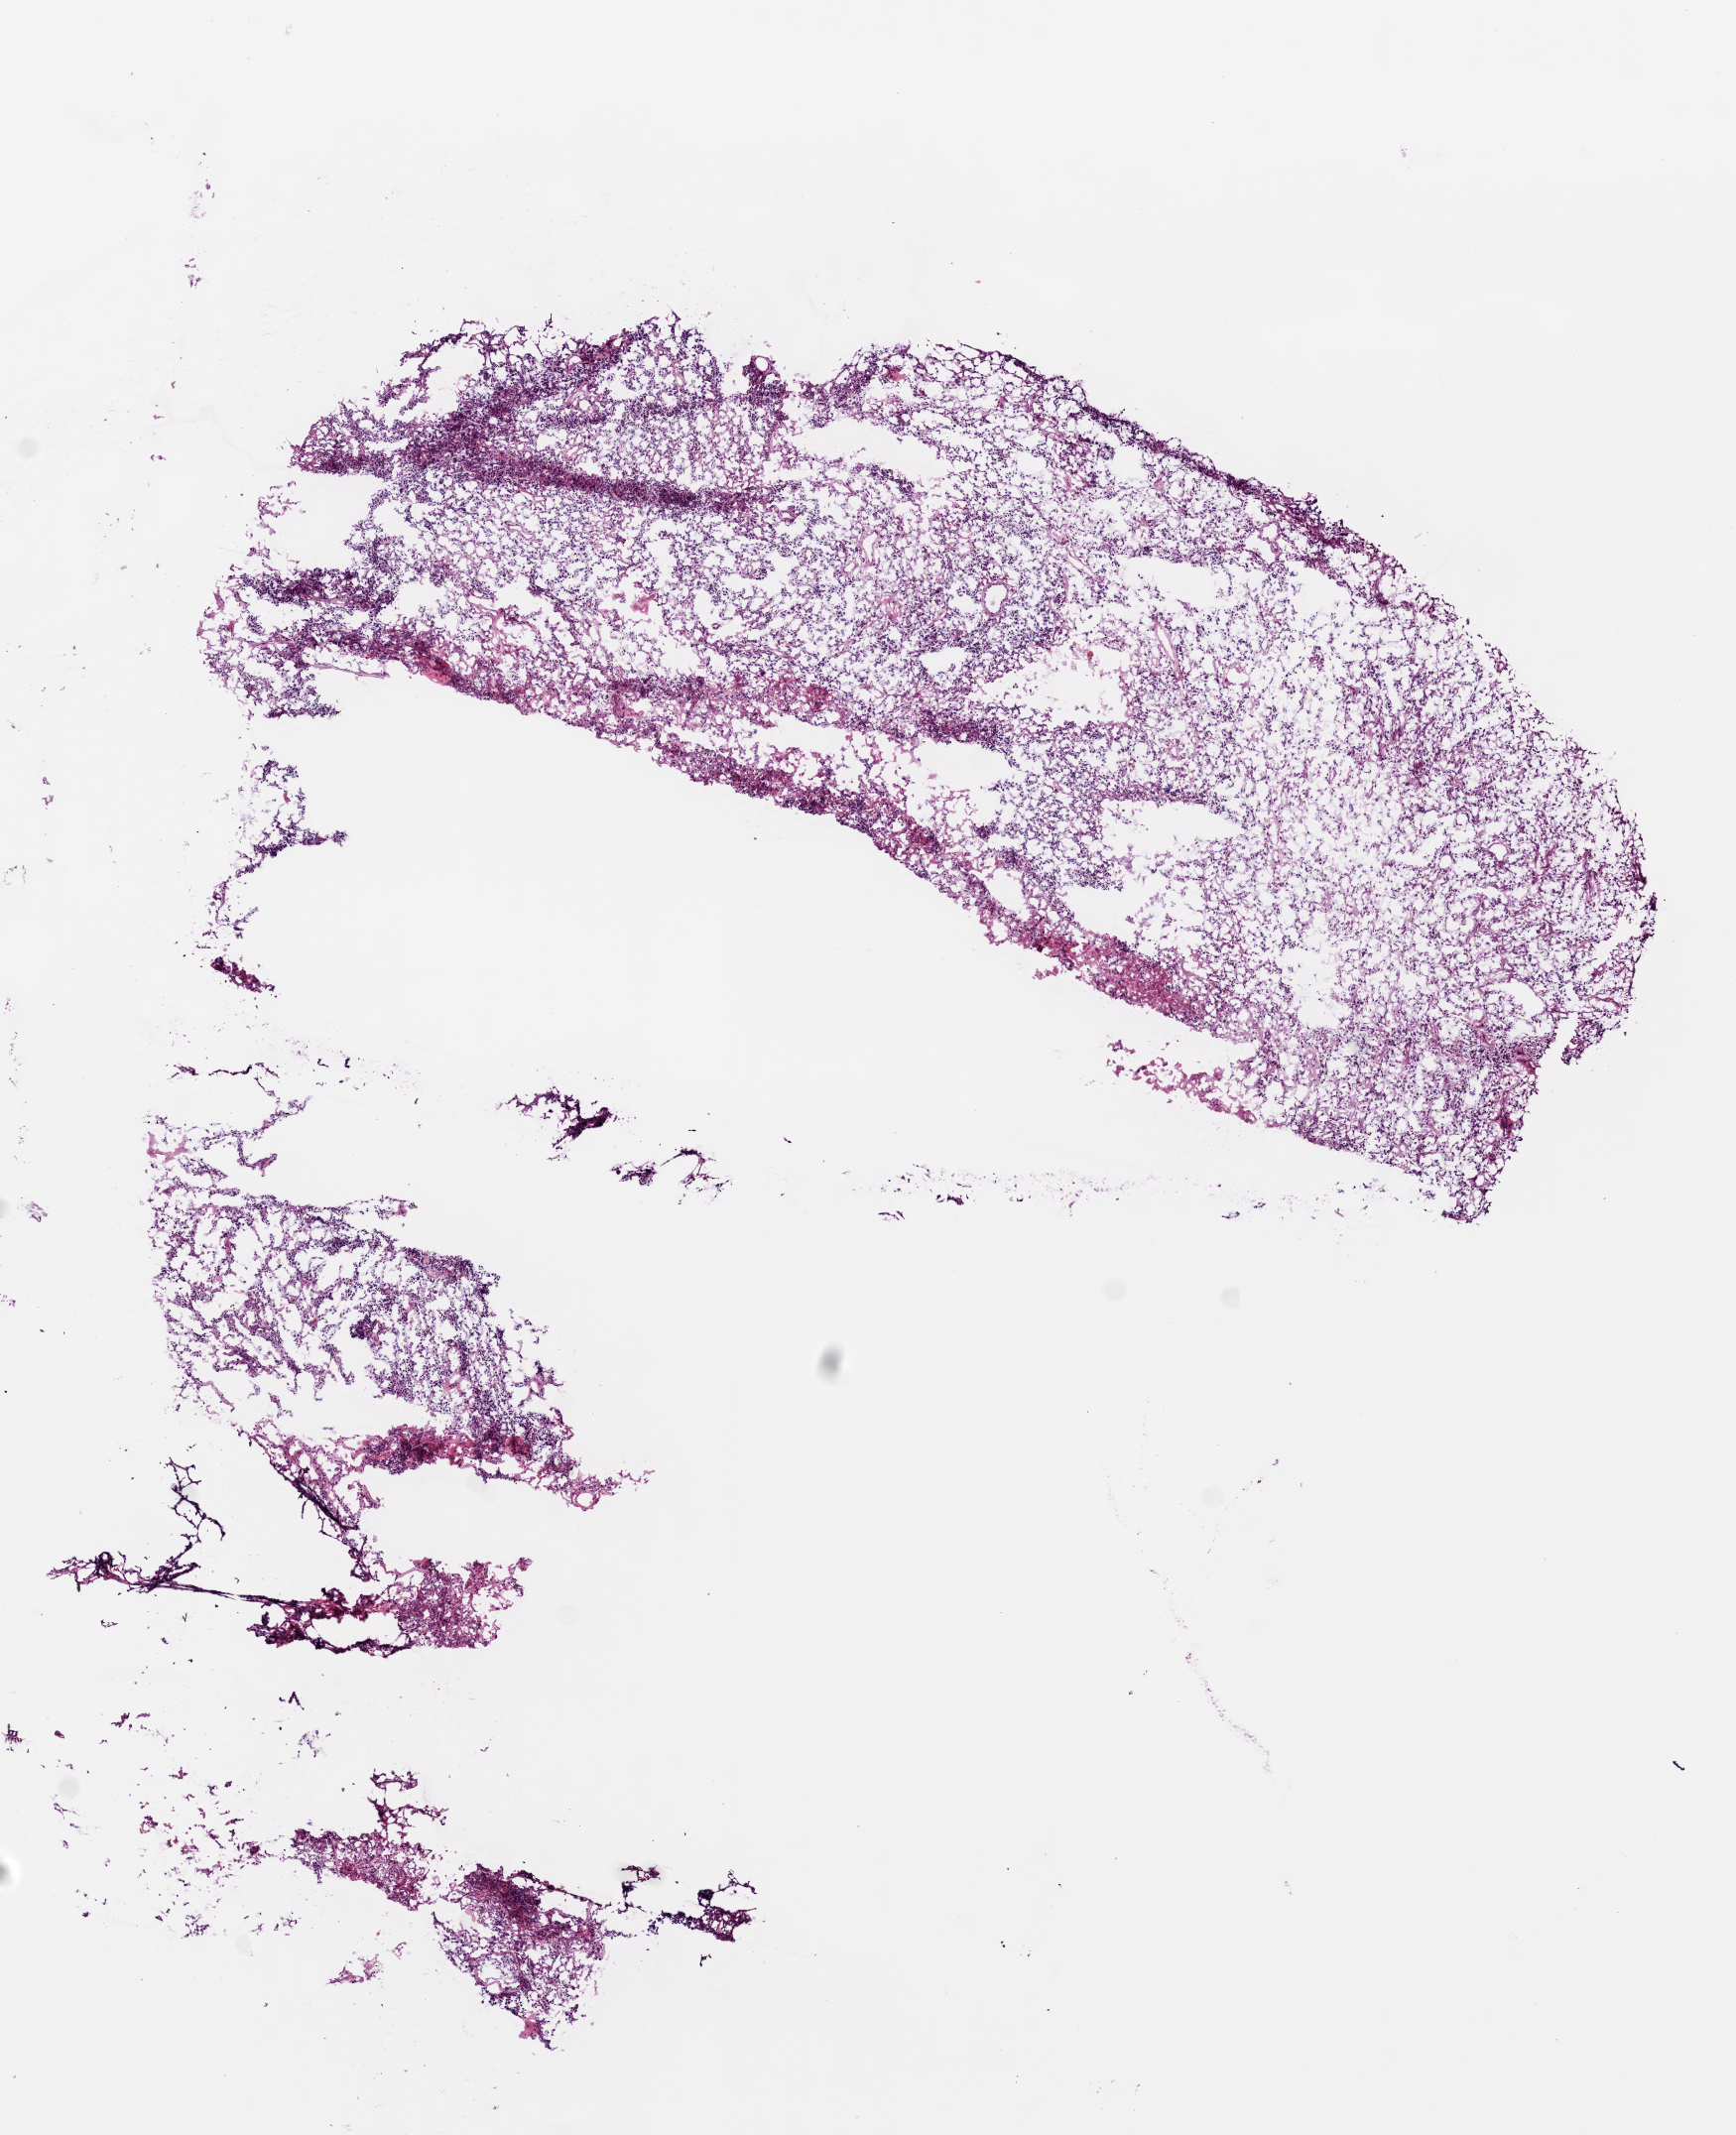
H&E-stained whole-slide image, shown as a low-resolution overview of the whole scanned area (about 7.0 x 8.6 mm); frozen section; sample: primary tumour, brain. Patient: male, age at initial diagnosis 70 years. Composition of this section per pathologist review: tumour cells 95%, tumour nuclei 80%, normal cells 0%, stromal cells 0%, necrosis 5%.
Histologic diagnosis: Glioblastoma.